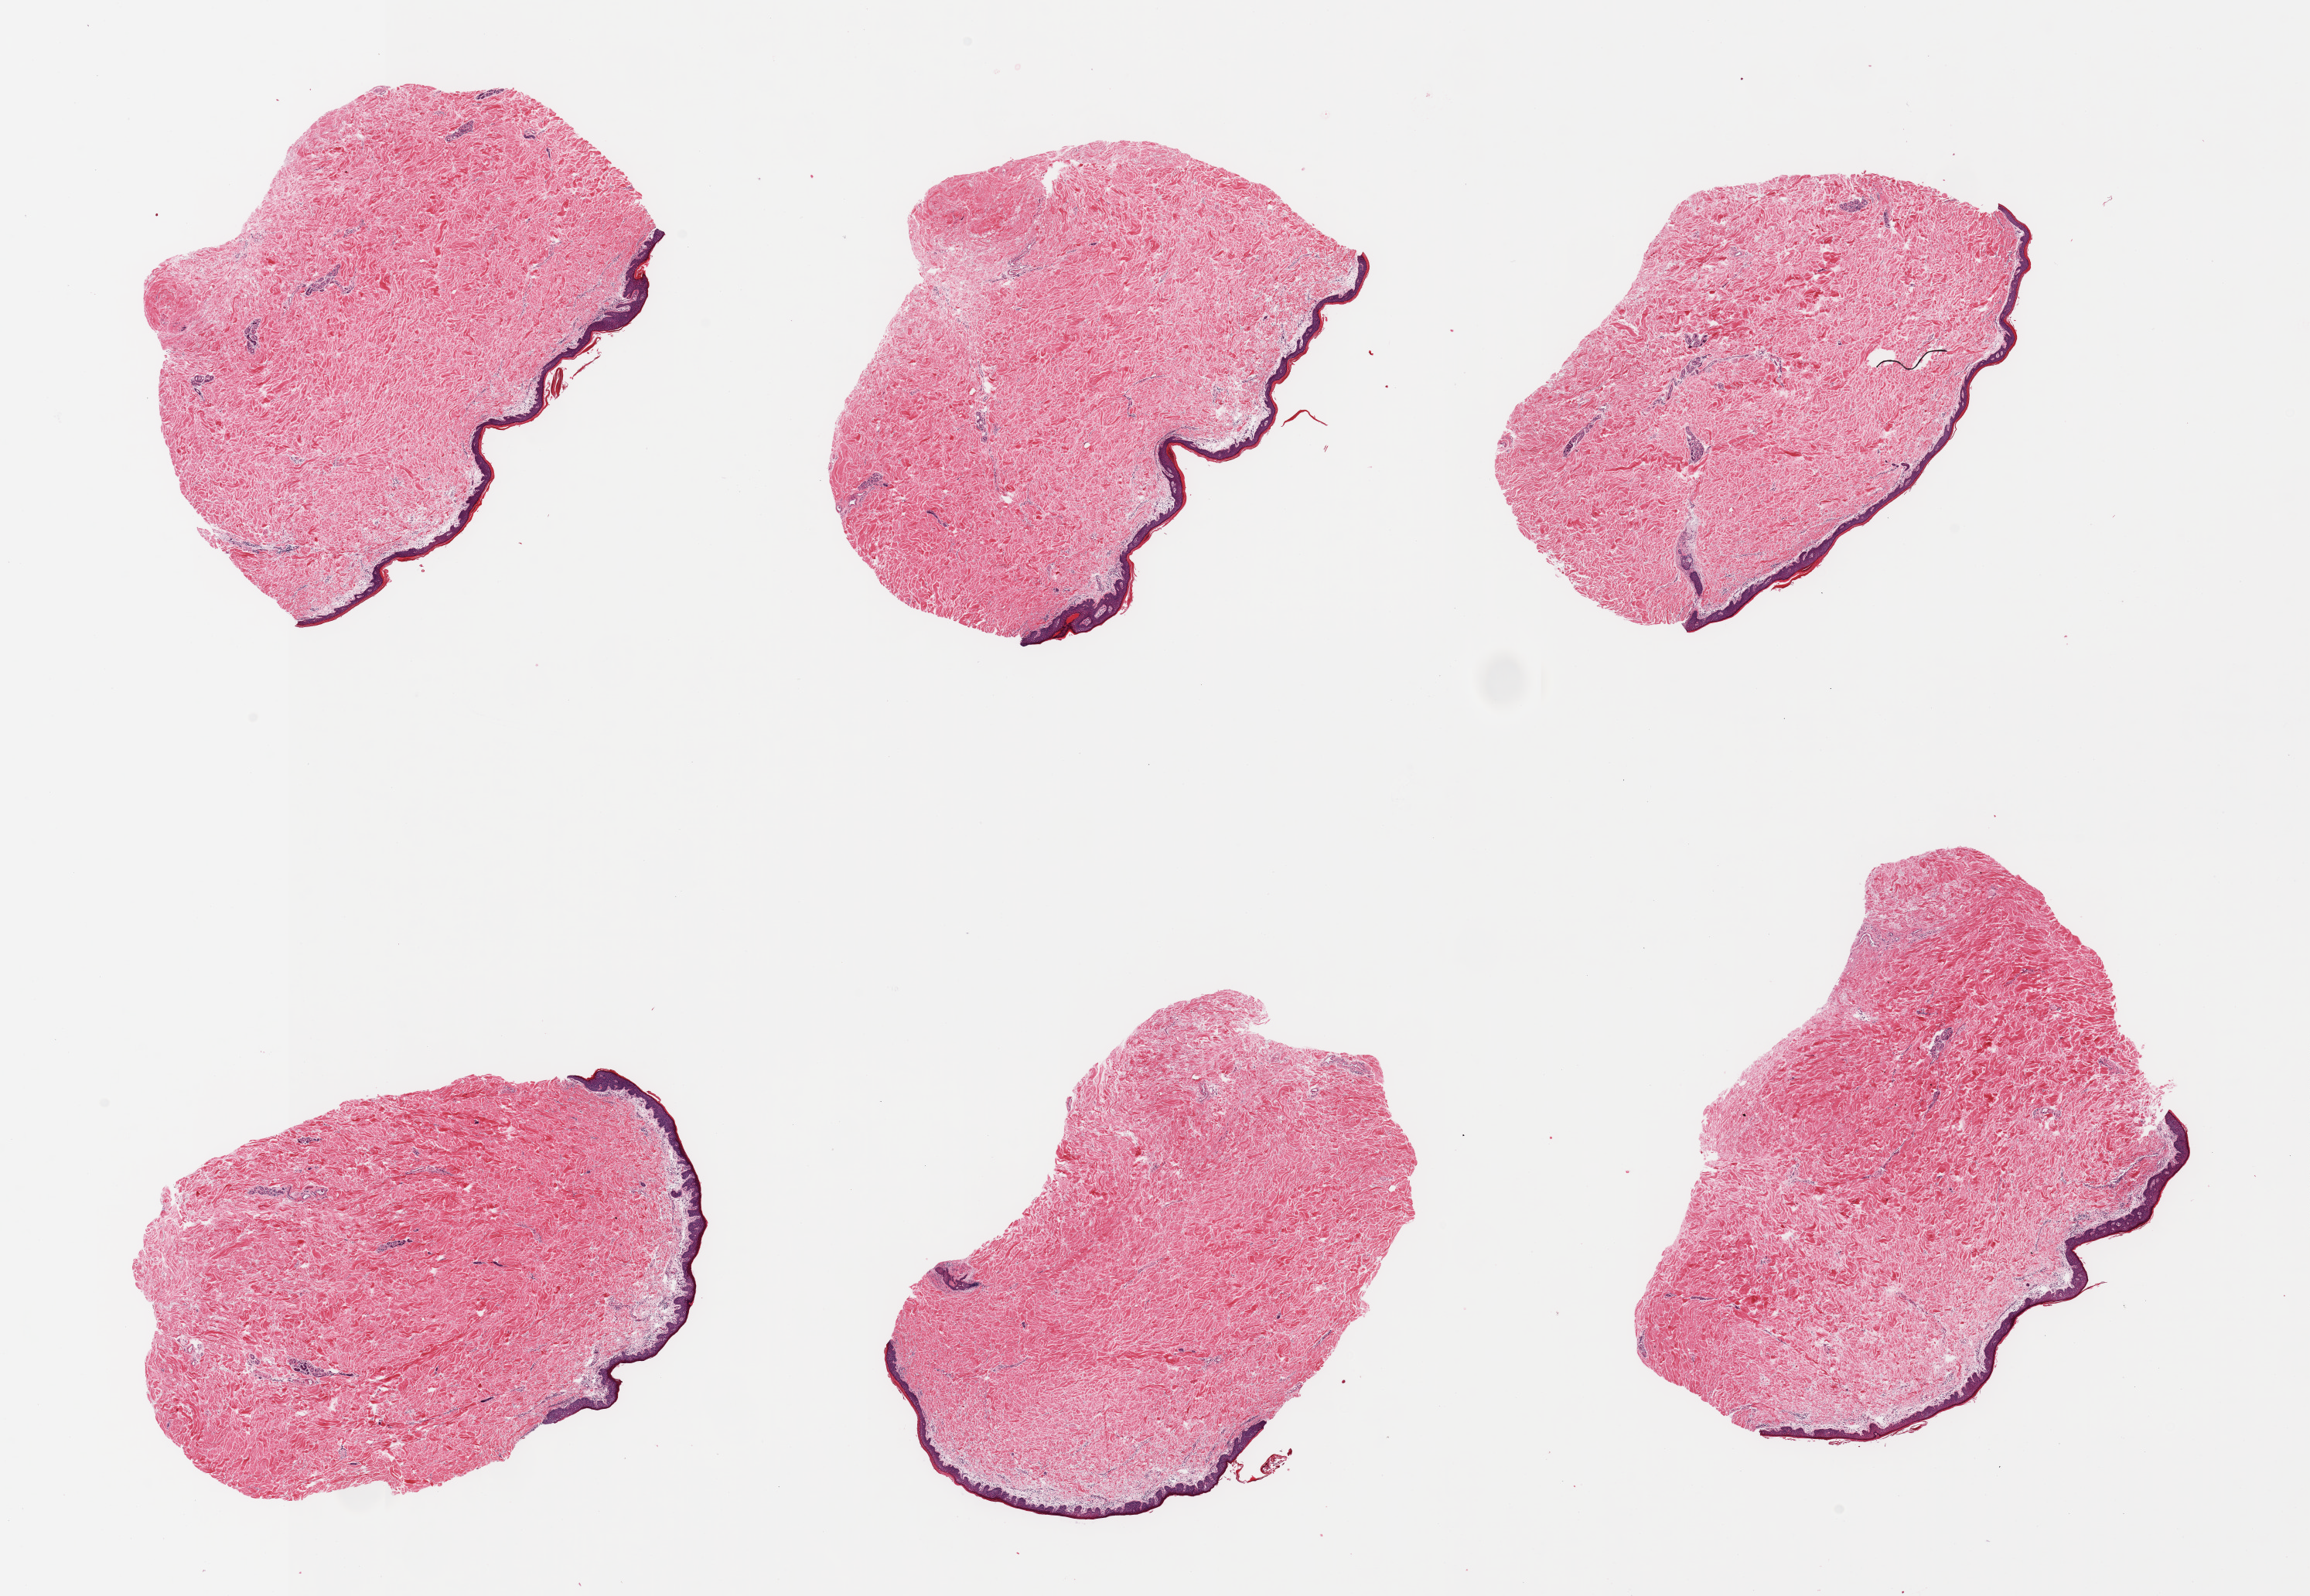
H&E whole-slide image, brightfield — whole scanned area (about 23.6 x 16.3 mm, from a 20x scan) shown as a low-resolution overview; PAXgene-fixed paraffin-embedded (PFPE) section; target tissue: skin of suprapubic region; donor tissue sample. Male donor.
Review note (as recorded): 6 pieces, no significant dermal fat; squamous epithelium is ~50-60 microns.